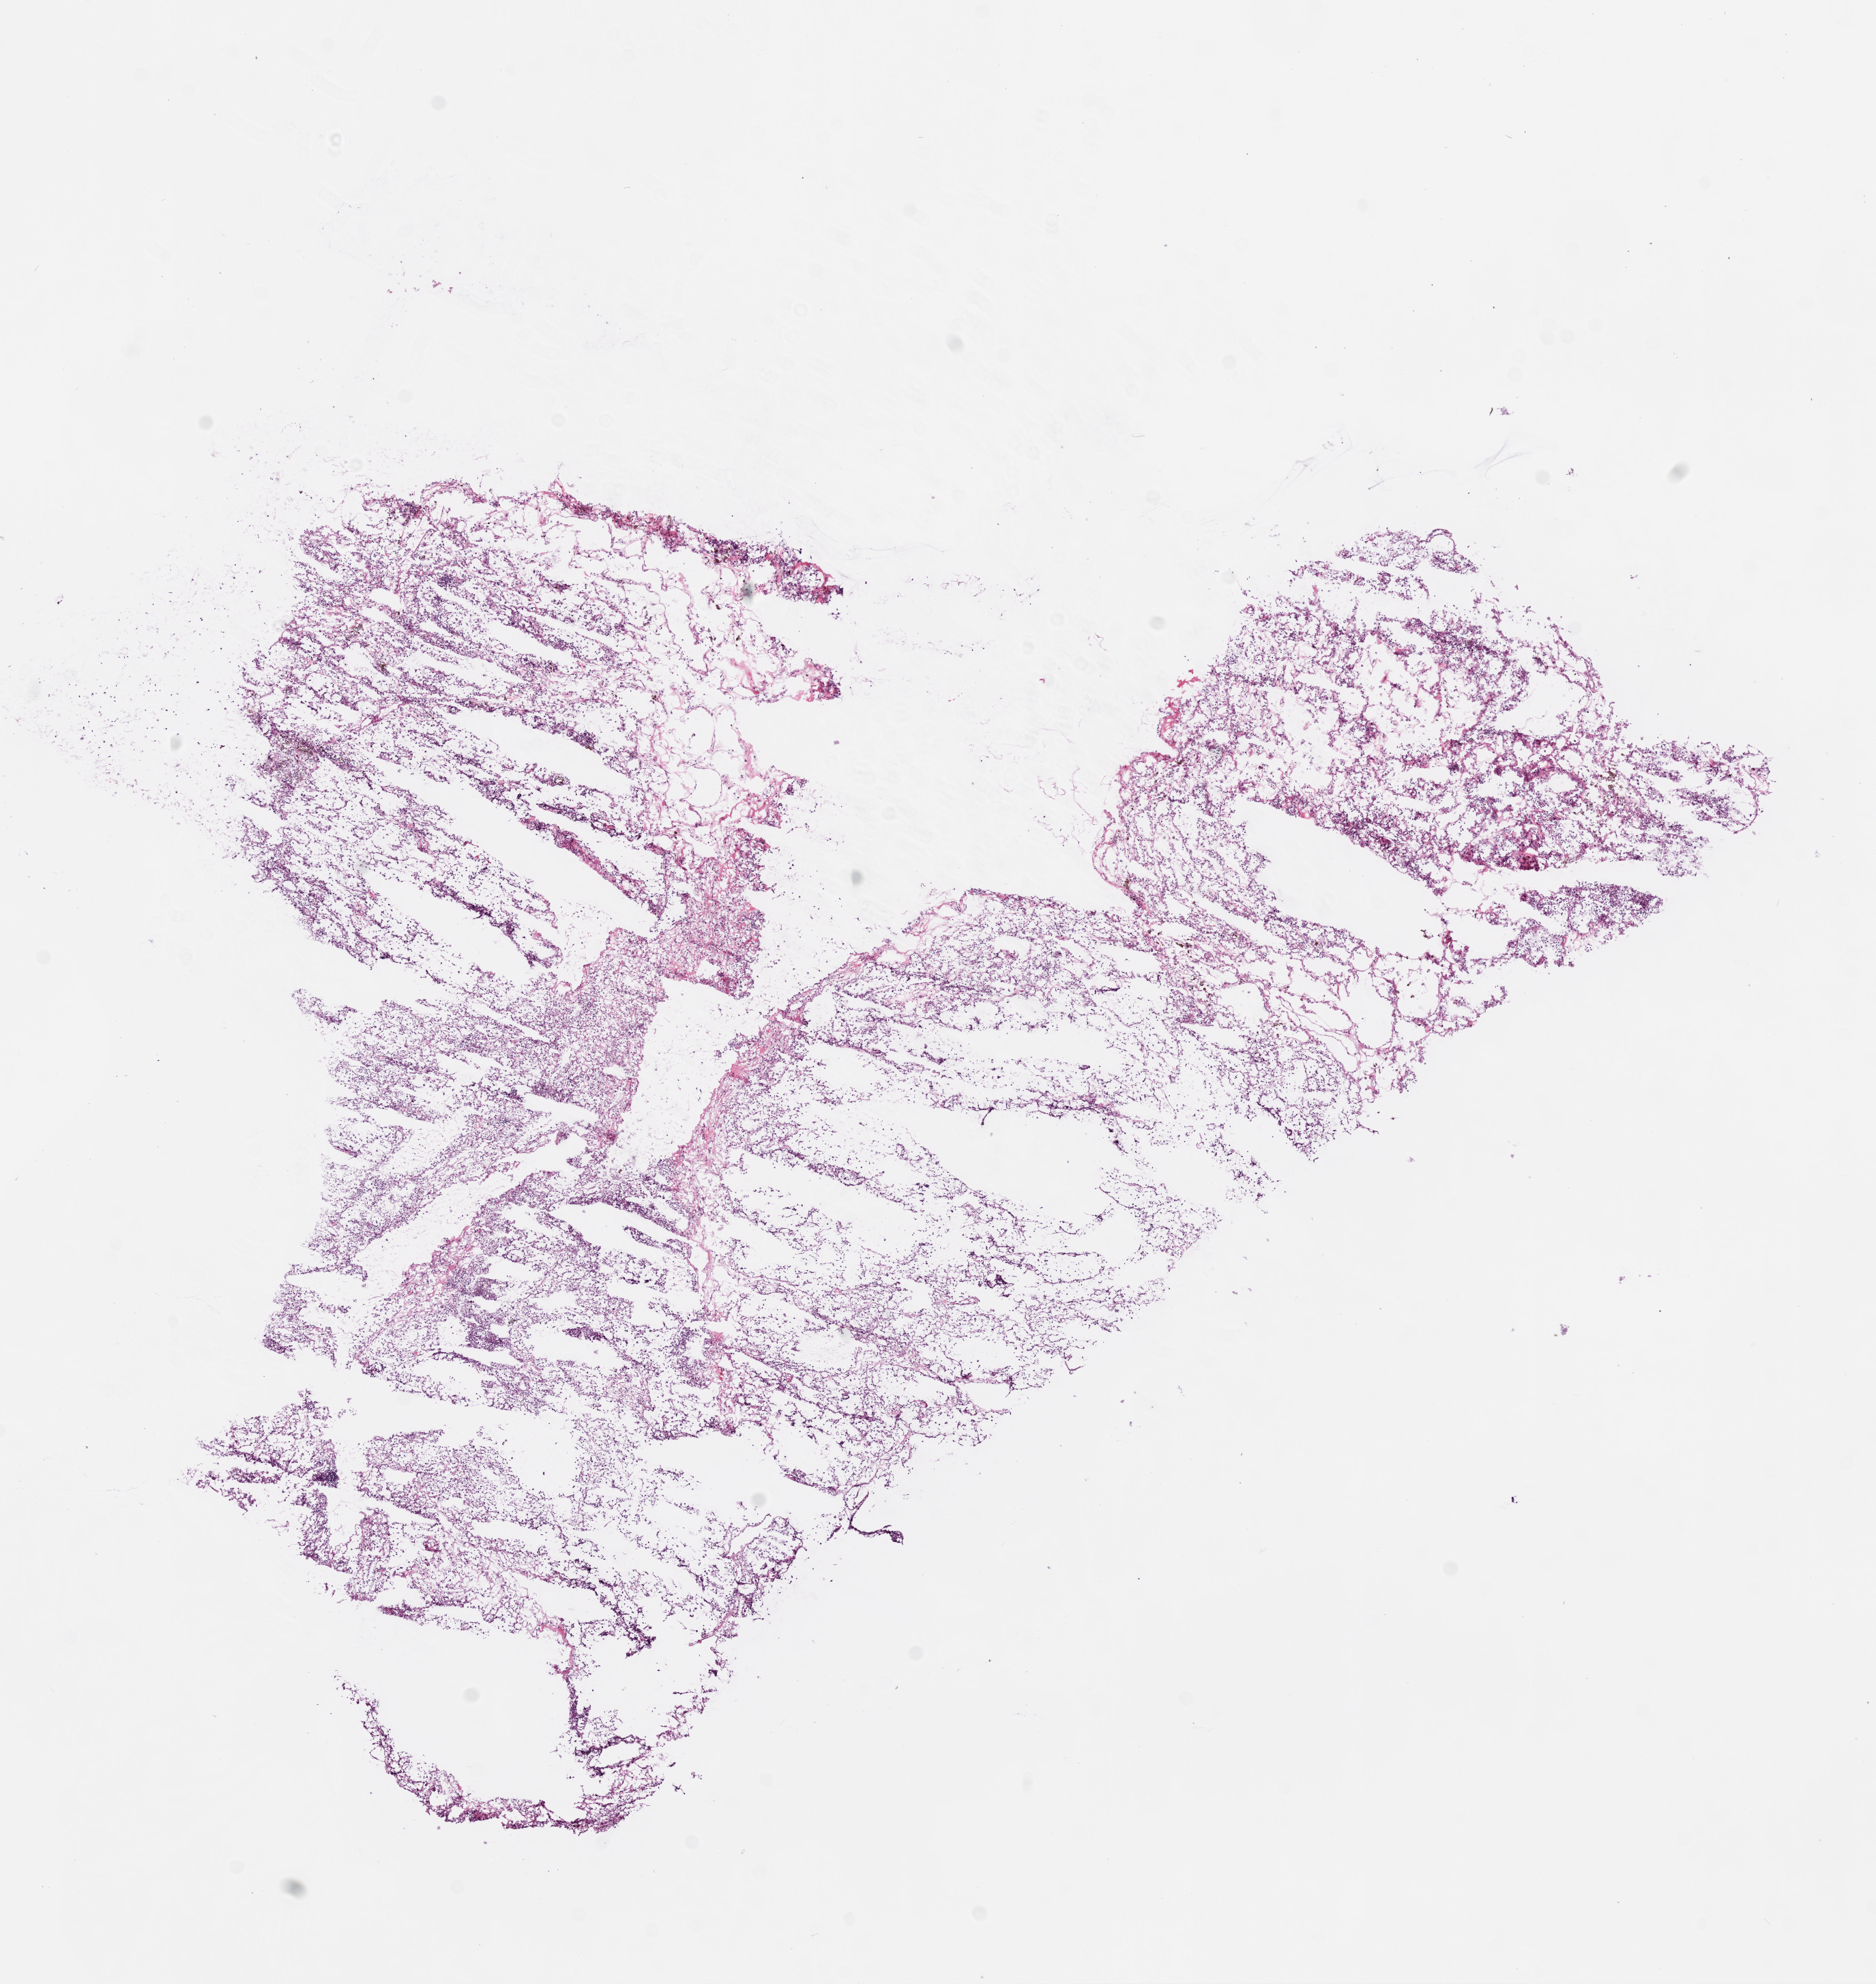
Digitized Hematoxylin and eosin (H&E) stained tissue section (whole slide), shown as a low-resolution overview of the whole scanned area (about 11.0 x 11.7 mm, from a 20x scan); frozen section from the bottom of the tissue portion; sample: primary tumour, kidney. Patient: female, age at initial diagnosis 57 years. Histologic grade: G2 (moderately differentiated). Pathologist review of this section (percent, as recorded): tumour cells 95%, tumour nuclei 60%, normal cells 0%, stromal cells 5%, necrosis 0%.
Pathologic diagnosis: Clear cell adenocarcinoma, NOS. Laterality: left. AJCC pathologic stage: I.